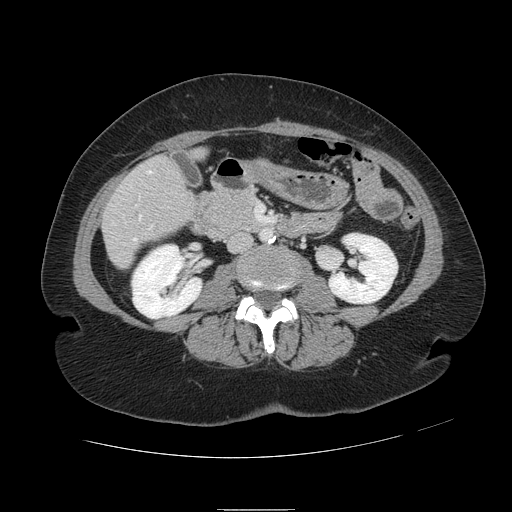
Contrast-enhanced abdominal CT, one axial slice; slice 25 of 121 in the series (ordered by position); 120 kVp; soft-tissue window (W 400 / L 40 HU); 512 × 512 image matrix. Female patient, age 52 years. From the clinical record (not read from this slice): diagnosis: colorectal cancer liver metastases, imaged before liver resection; multiple liver metastases: yes; largest metastasis: 6.3 cm; chemotherapy before resection: yes.
Annotated regions visible in this slice (outlined manually by an expert reader):
- hepatic veins: bounding box <133,171,152,240> (left, top, right, bottom; pixels)
- liver: <103,150,206,268>
- planned liver remnant (the part of the liver to remain after resection): <194,151,206,158>